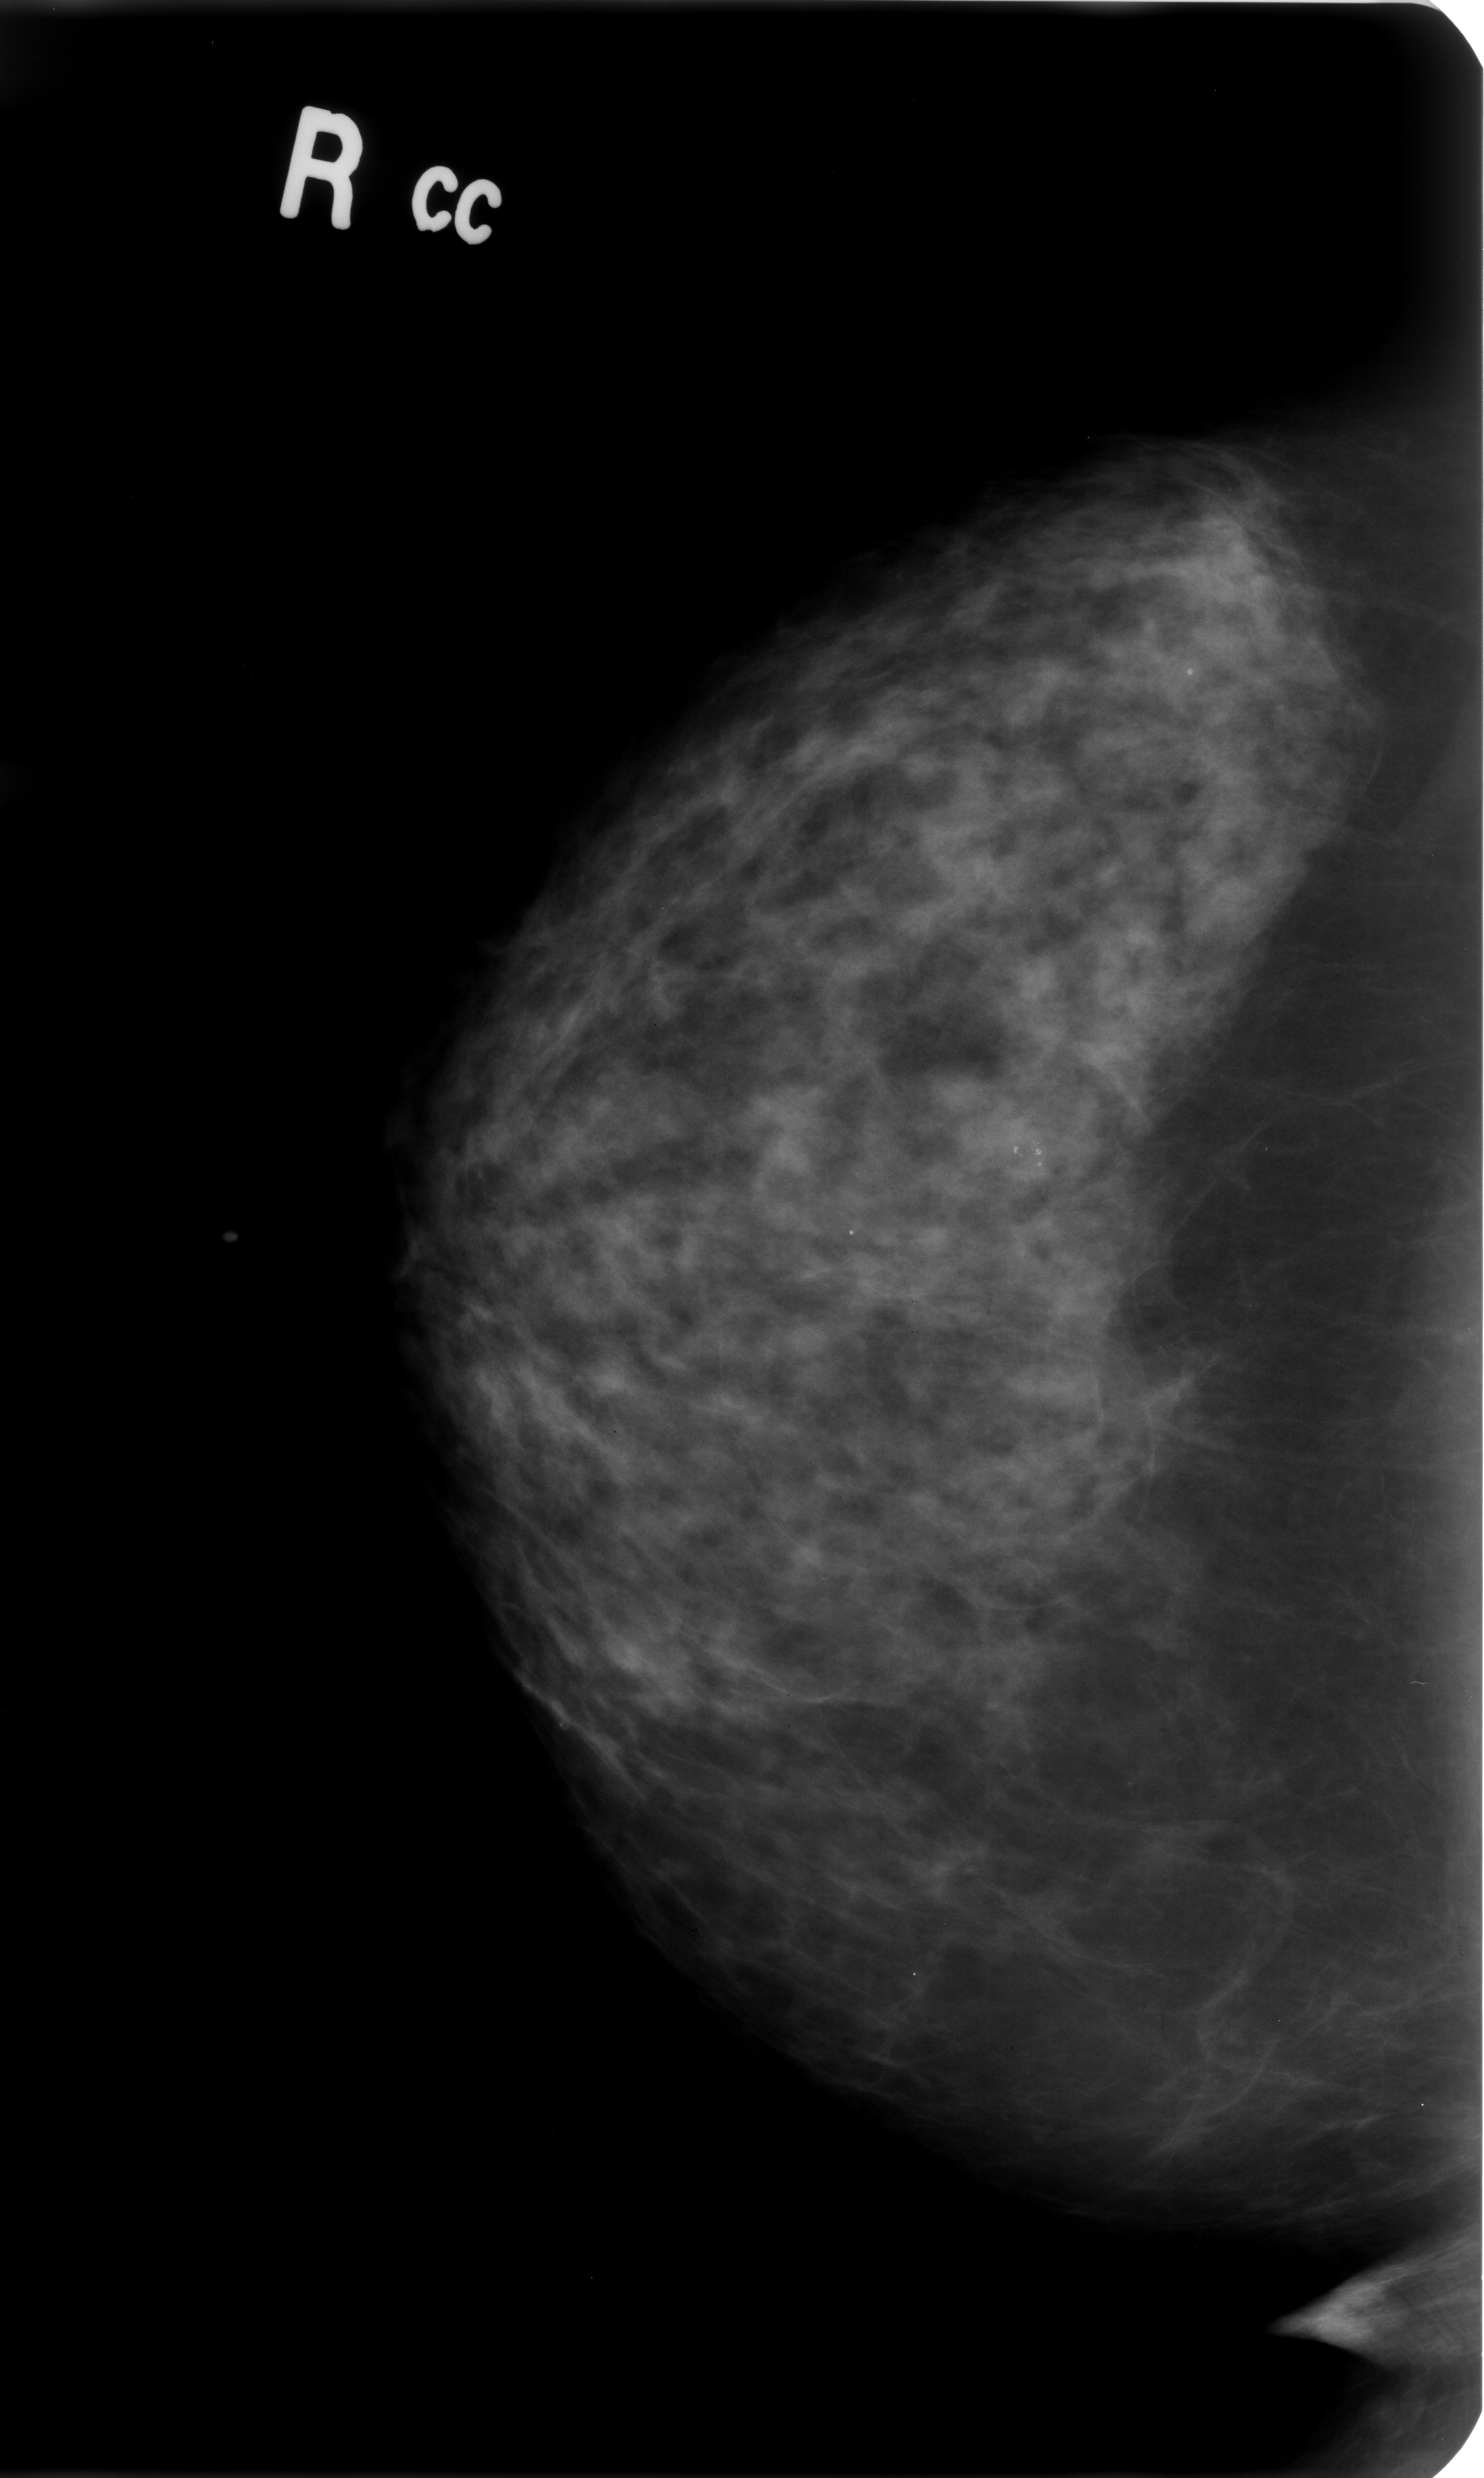
Digitized screen-film mammogram; right breast; craniocaudal (CC) view; BI-RADS breast density category 3 (scale 1–4); 1484 × 2478 image matrix.
Expert-marked regions of interest on this image (one box per marked abnormality):
- calcifications, morphology pleomorphic, distribution clustered; BI-RADS assessment category 4; subtlety rating 4 on a 1 (subtle) to 5 (obvious) scale; pathology result (as recorded, not read from the image): benign: box from (x=976, y=1098) to (x=1091, y=1217) px